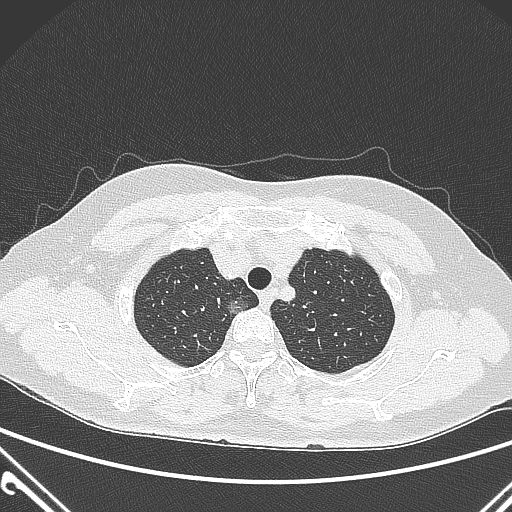
Chest CT, one axial slice. Position 240 of 300 along the scan axis. 120 kVp. Lung window (W 1500 / L -600 HU). 512 × 512 image matrix, field of view 350 × 350 mm. Female patient, age 54 years. From the clinical record (not read from this slice): clinical TNM (as recorded): T1a N0 M0.
Annotated regions visible in this slice (bounding box drawn by a radiologist):
- lung tumour (recorded histology: adenocarcinoma): bounding box [x1, y1, x2, y2] px = [223, 292, 251, 321]